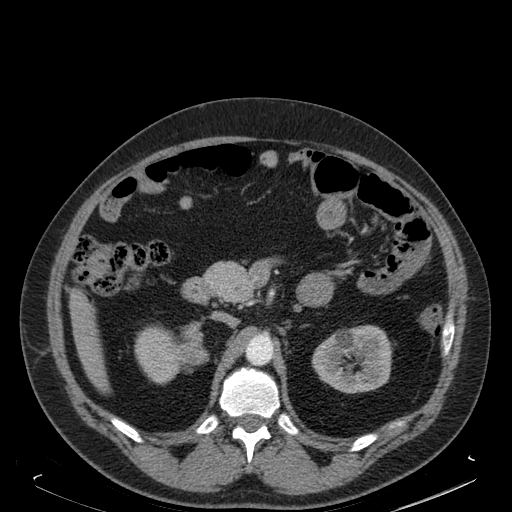
Contrast-enhanced abdominal CT, one axial slice; slice 101 of 181 in the series (ordered by position); soft-tissue window (W 400 / L 40 HU); 512 × 512 image matrix. Male patient. From the clinical record (not read from this slice): diagnosis: adrenocortical carcinoma; tumour side: right adrenal; tumour size at pathology: 7.5 cm; Ki-67 index: 25 %; stage (as recorded): 4.
Structures marked on this image (semi-automatic segmentation, software-assisted and operator-edited):
- mass: bounding box (x1, y1, x2, y2) in pixels: (183, 325, 206, 364)